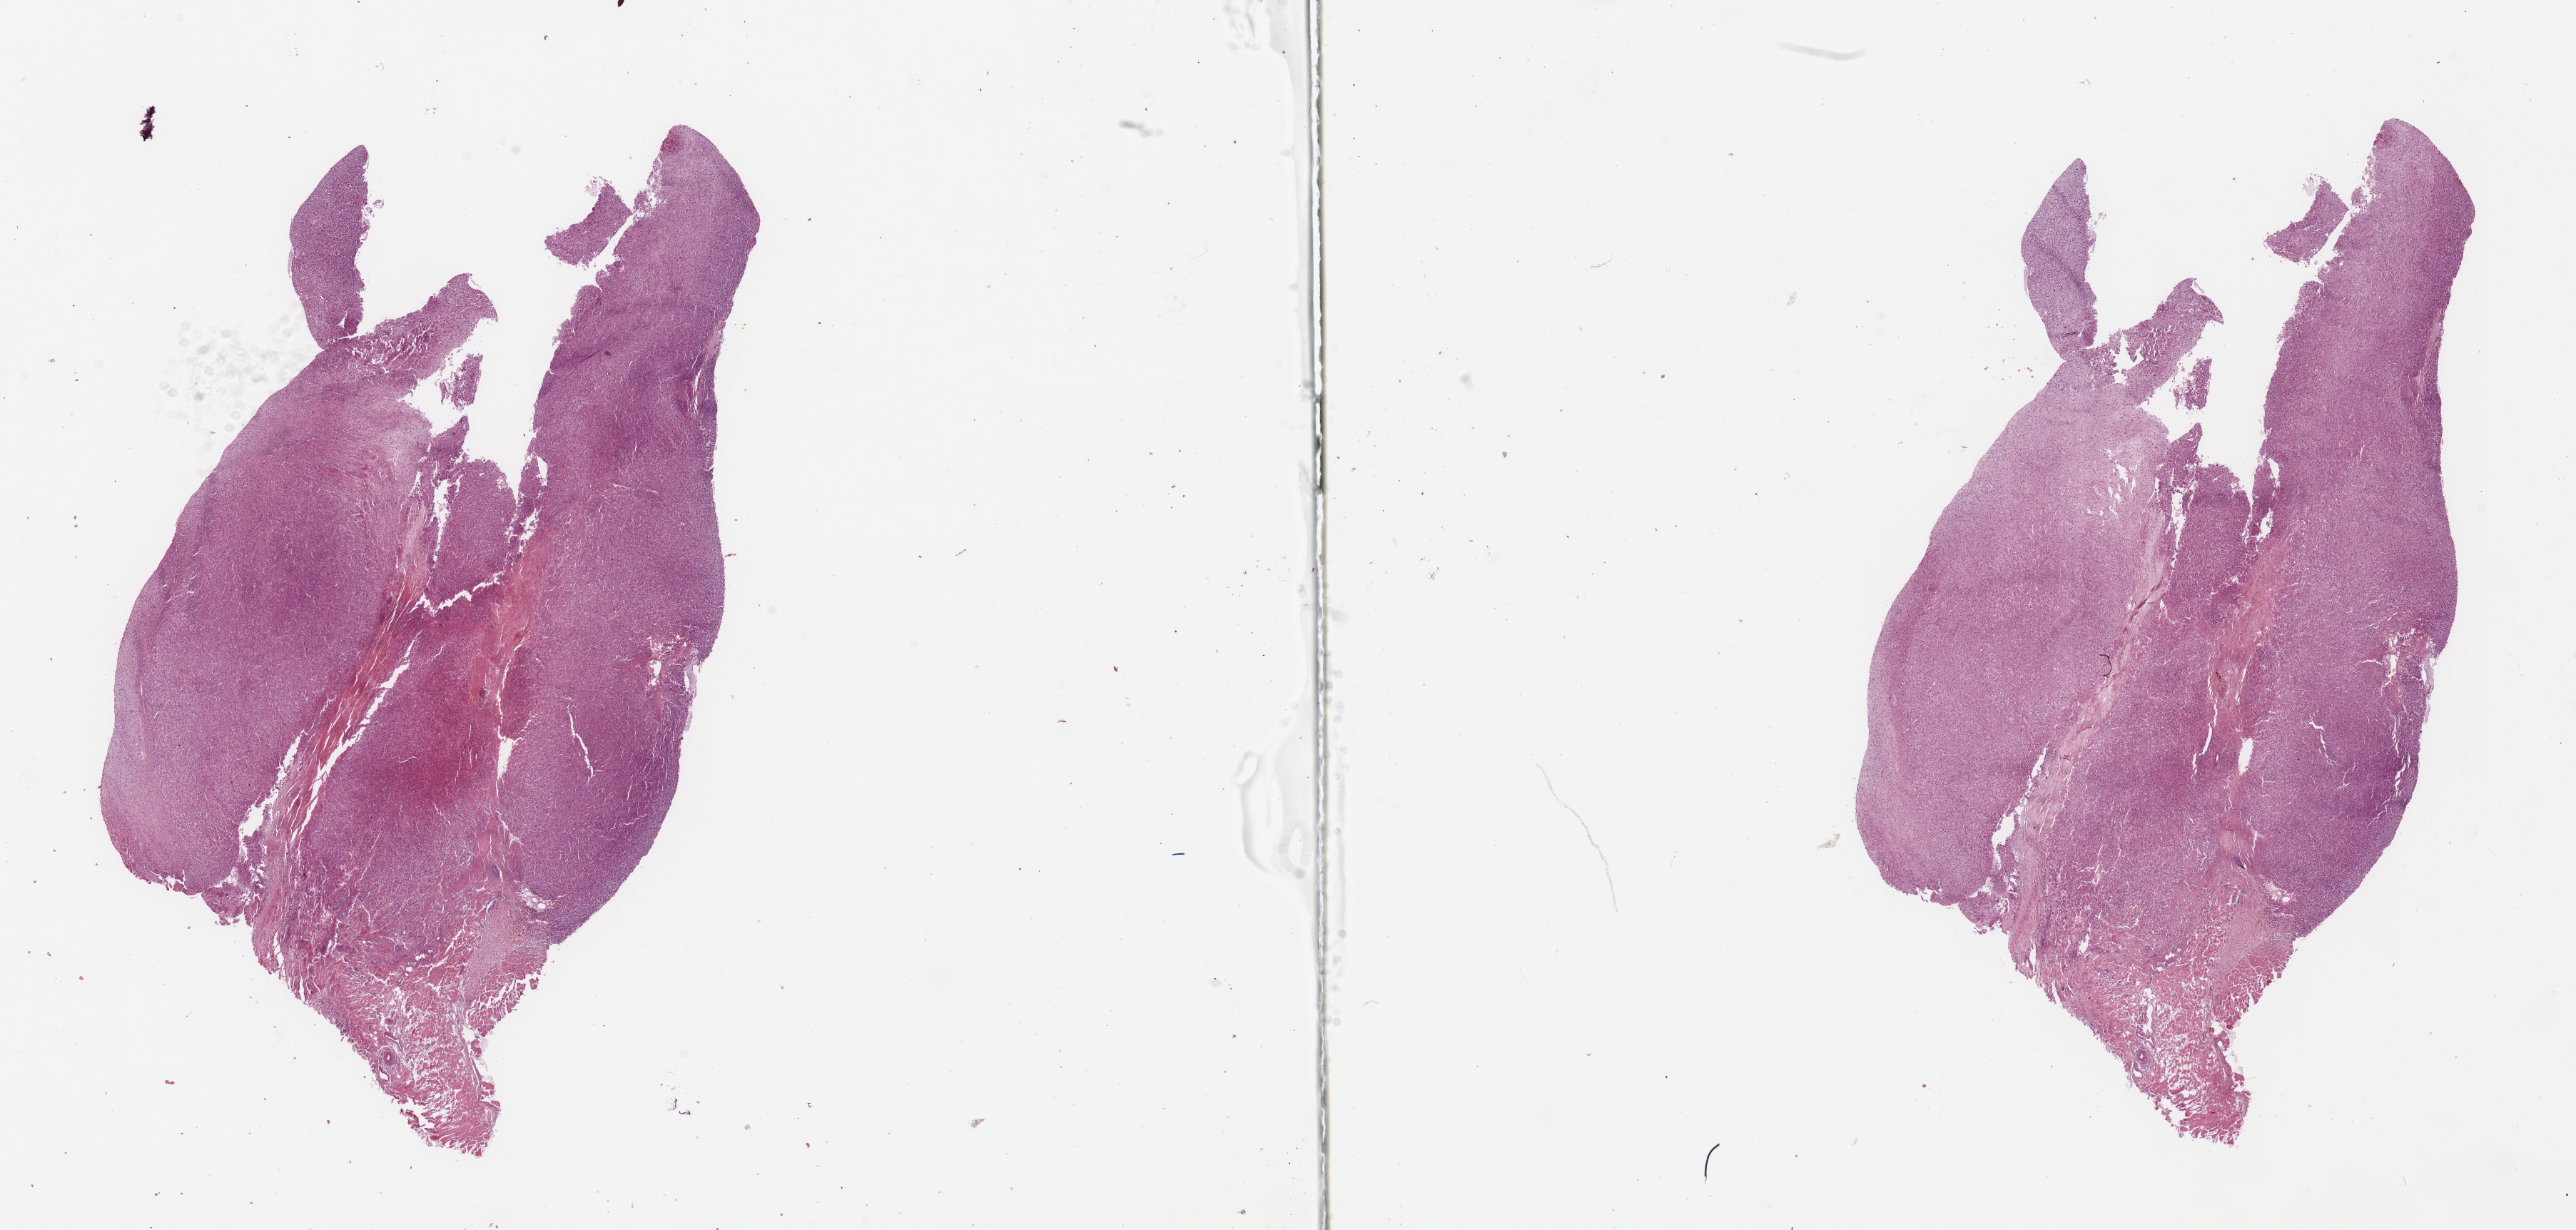
H&E whole-slide image — whole scanned area (about 28.5 x 13.6 mm, slide scanned at 20x) shown as a low-resolution overview, tumour tissue sample. Patient: female, age 50 years.
Primary tumour site (as recorded): lower extremity. Patient diagnosis (cohort enrolment): sarcoma (site not recorded at cohort level).